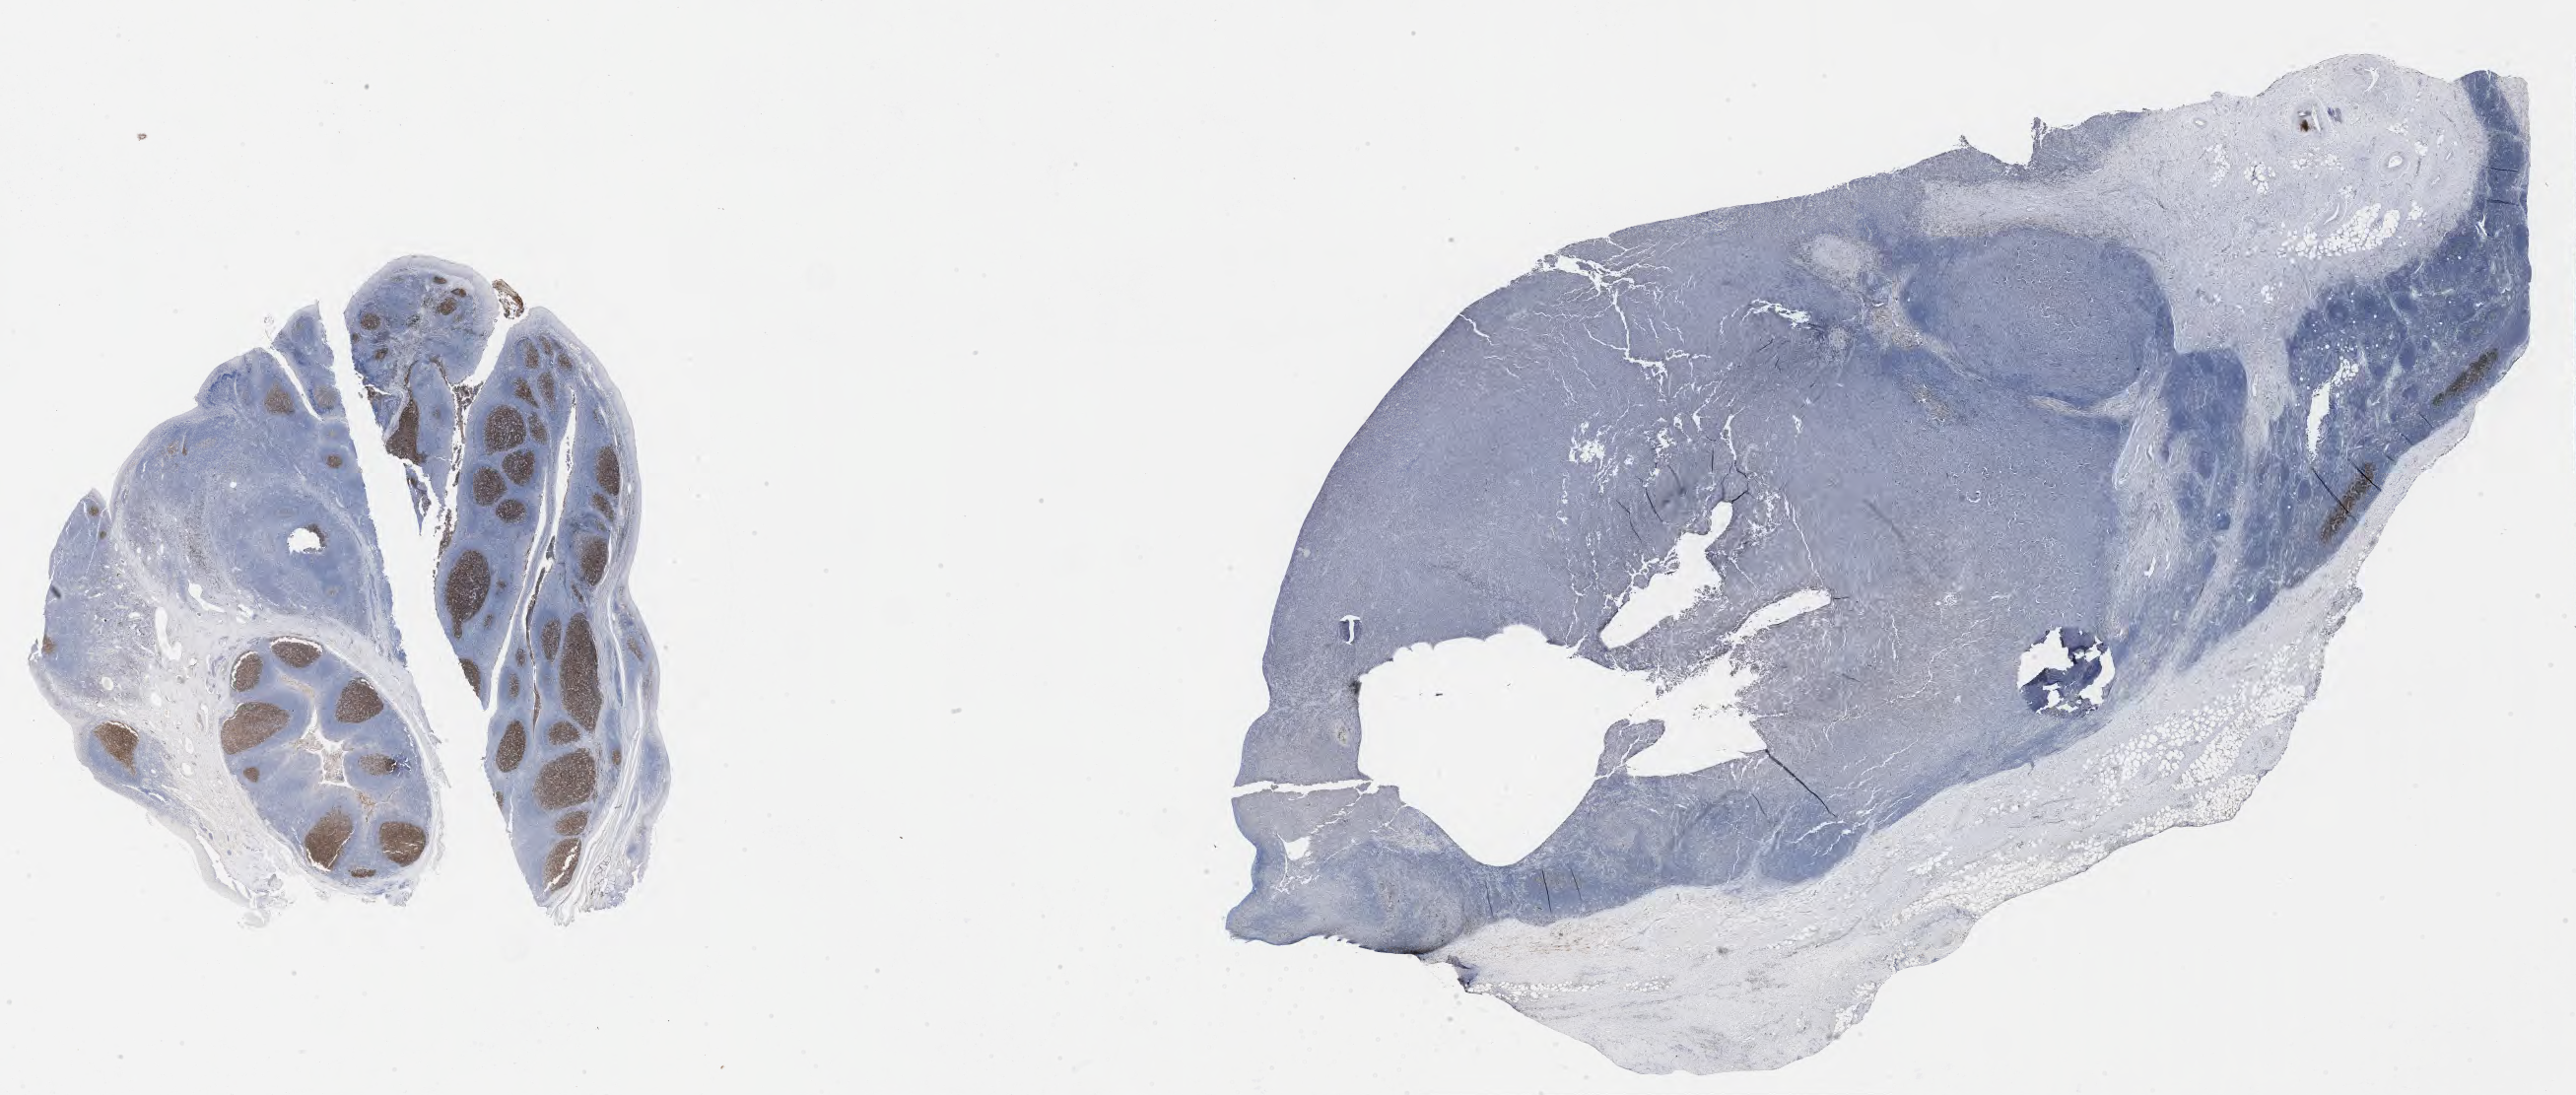
Whole-slide image, immunohistochemical stain for CD10, a low-resolution overview of the entire scanned area, about 42.3 x 18.0 mm. Specimen: tumor tissue. Site: lymph node. Male patient, aged 60.
- diagnosis: Diffuse large B-cell lymphoma, NOS